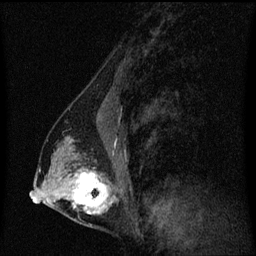
Breast MRI (dynamic contrast-enhanced), one sagittal slice; dynamic contrast-enhanced series, image 2 of 3 at this slice position (ordered by acquisition); 1.5 T; TE 4.2 ms, TR 8.4 ms; 2 mm slice thickness; 256 × 256 image matrix, field of view 200 × 200 mm. Patient: female, 40 years. From the clinical record (not read from this slice): setting: breast cancer imaged before/during neoadjuvant chemotherapy; receptor status: triple-negative.
Outlined on this slice (semi-automatically segmented with operator editing):
- analysis volume of interest (the breast-tissue region the enhancement analysis was run in; not a lesion): box from (x=44, y=128) to (x=120, y=221) px
- tumour enhancement mask (voxels above the 70 % enhancement threshold inside the analysis volume of interest): (x=72, y=172)–(x=113, y=215)